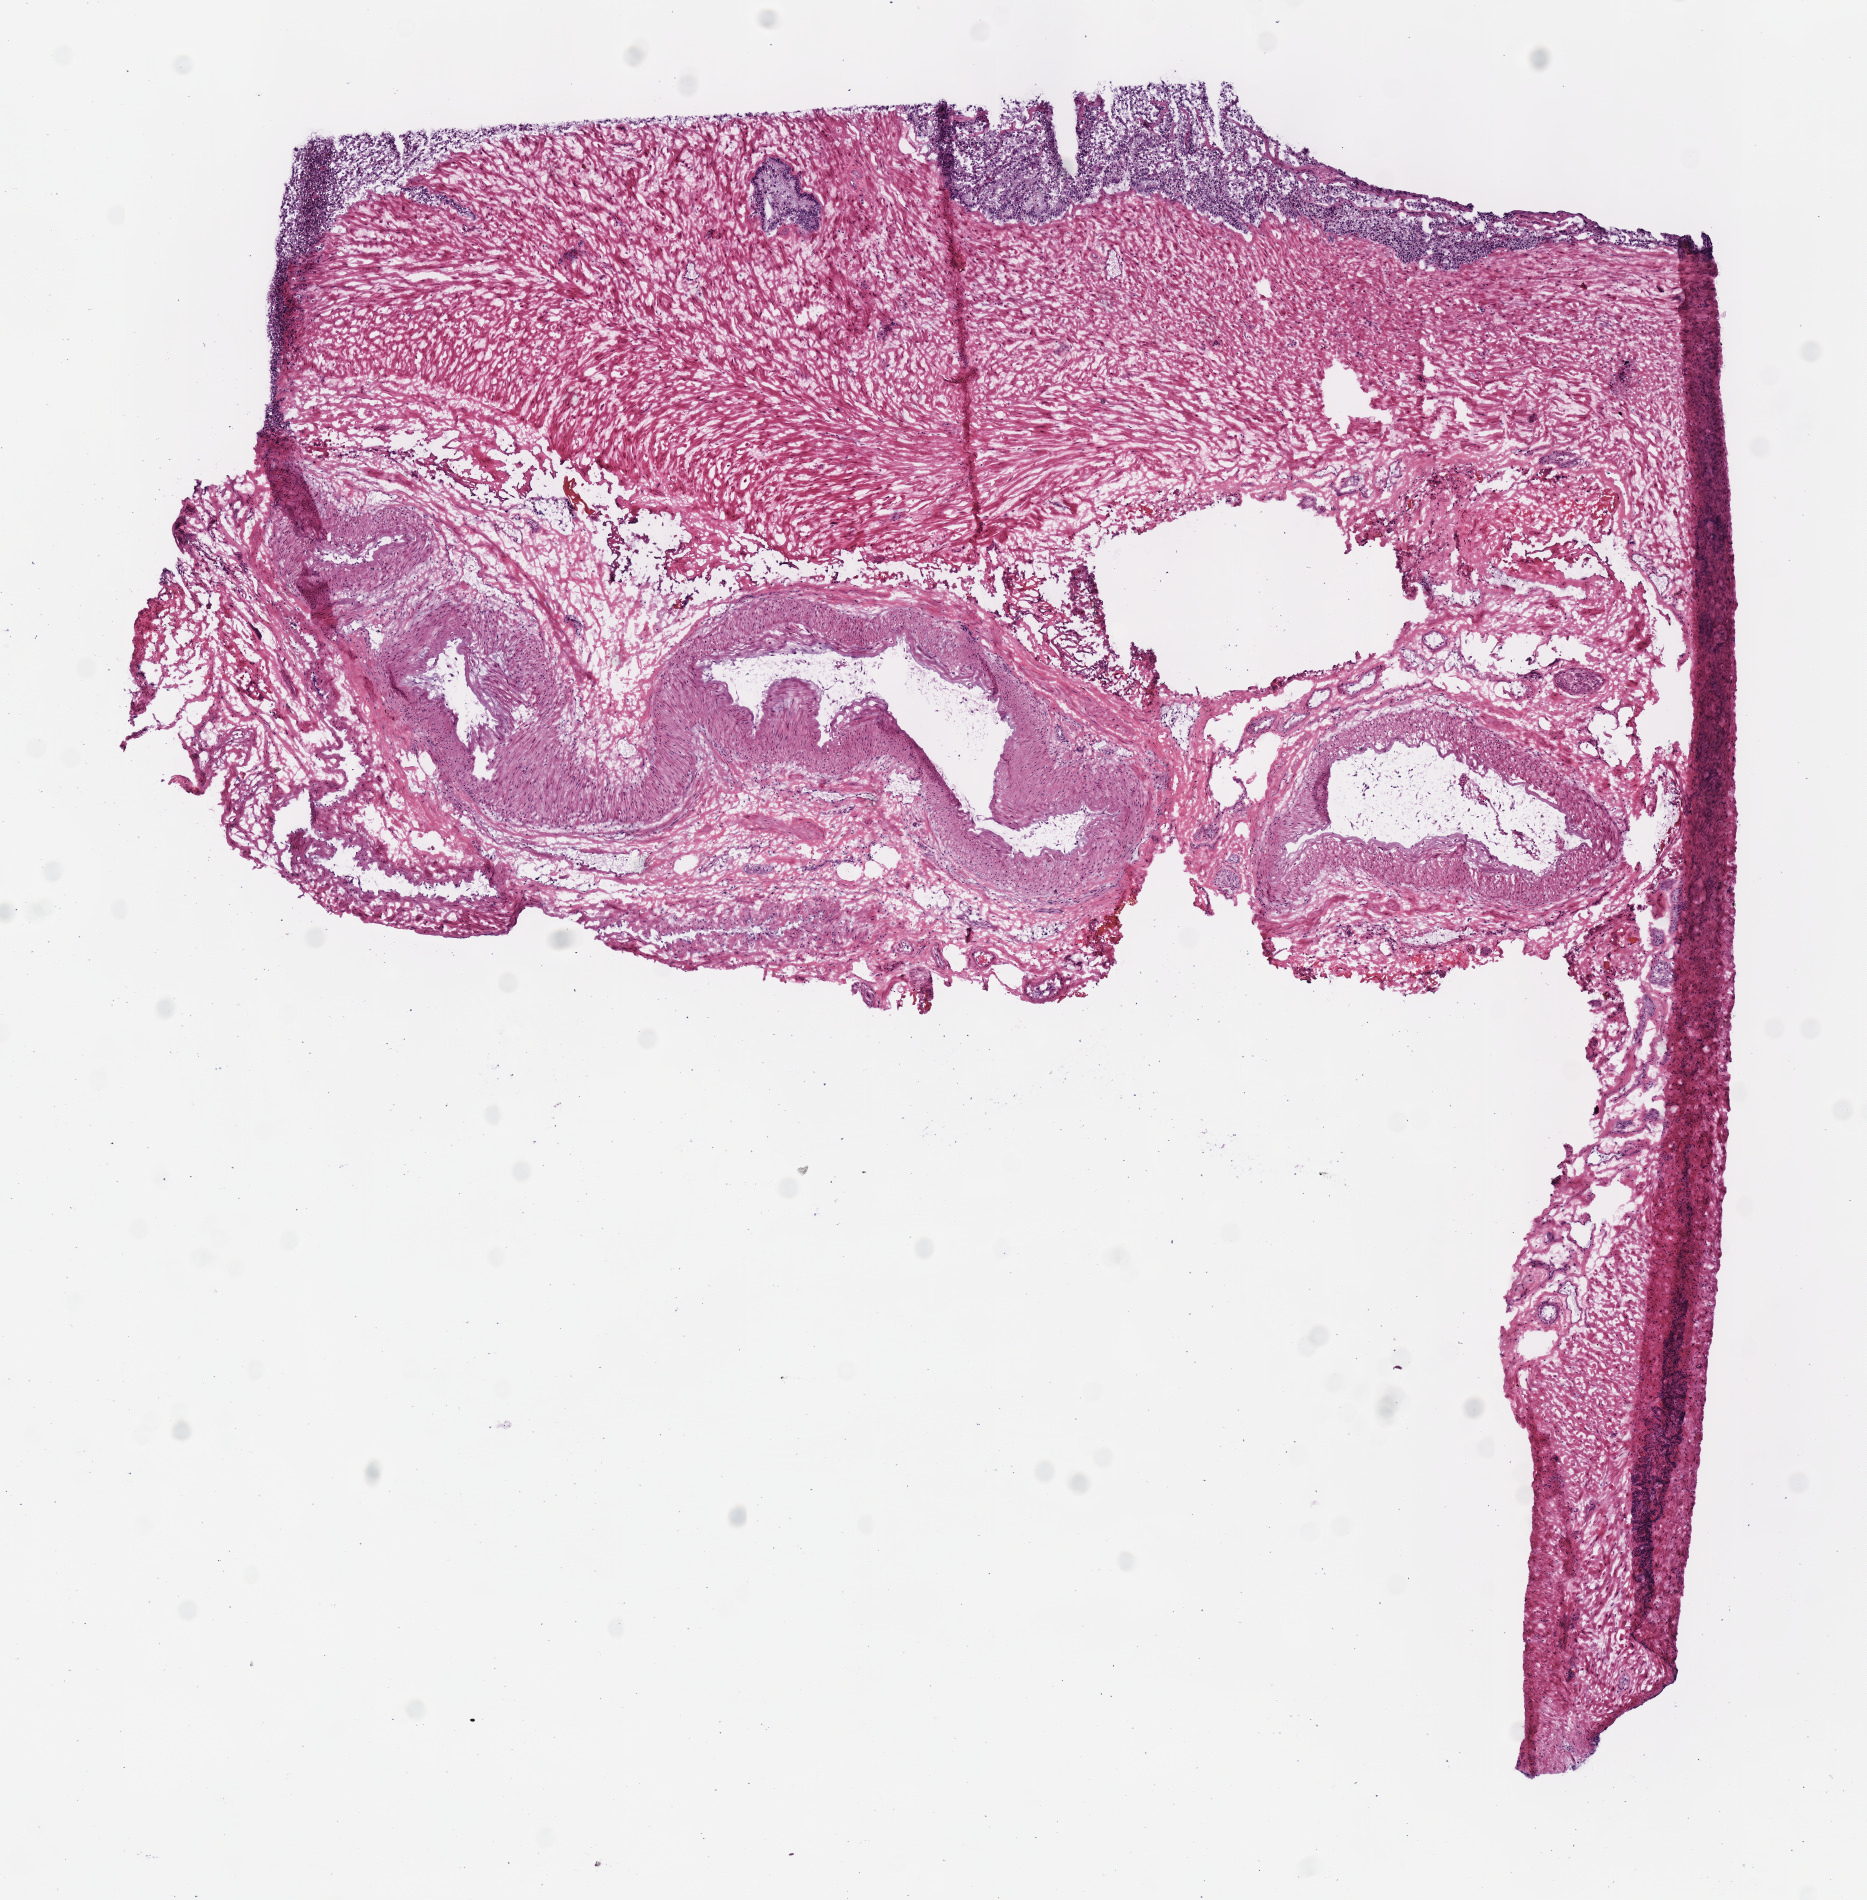
Digitized H&E-stained tissue section (whole slide) — low-resolution overview of the scanned area, about 7.3 x 7.5 mm; frozen section from the top of the tissue portion; prostate, solid tissue normal (non-tumour tissue) sample. Male patient; age at initial diagnosis 48 years.
- this section: solid tissue normal (non-tumour) sample from the same patient
- patient diagnosis: Acinar cell carcinoma (prostate gland)